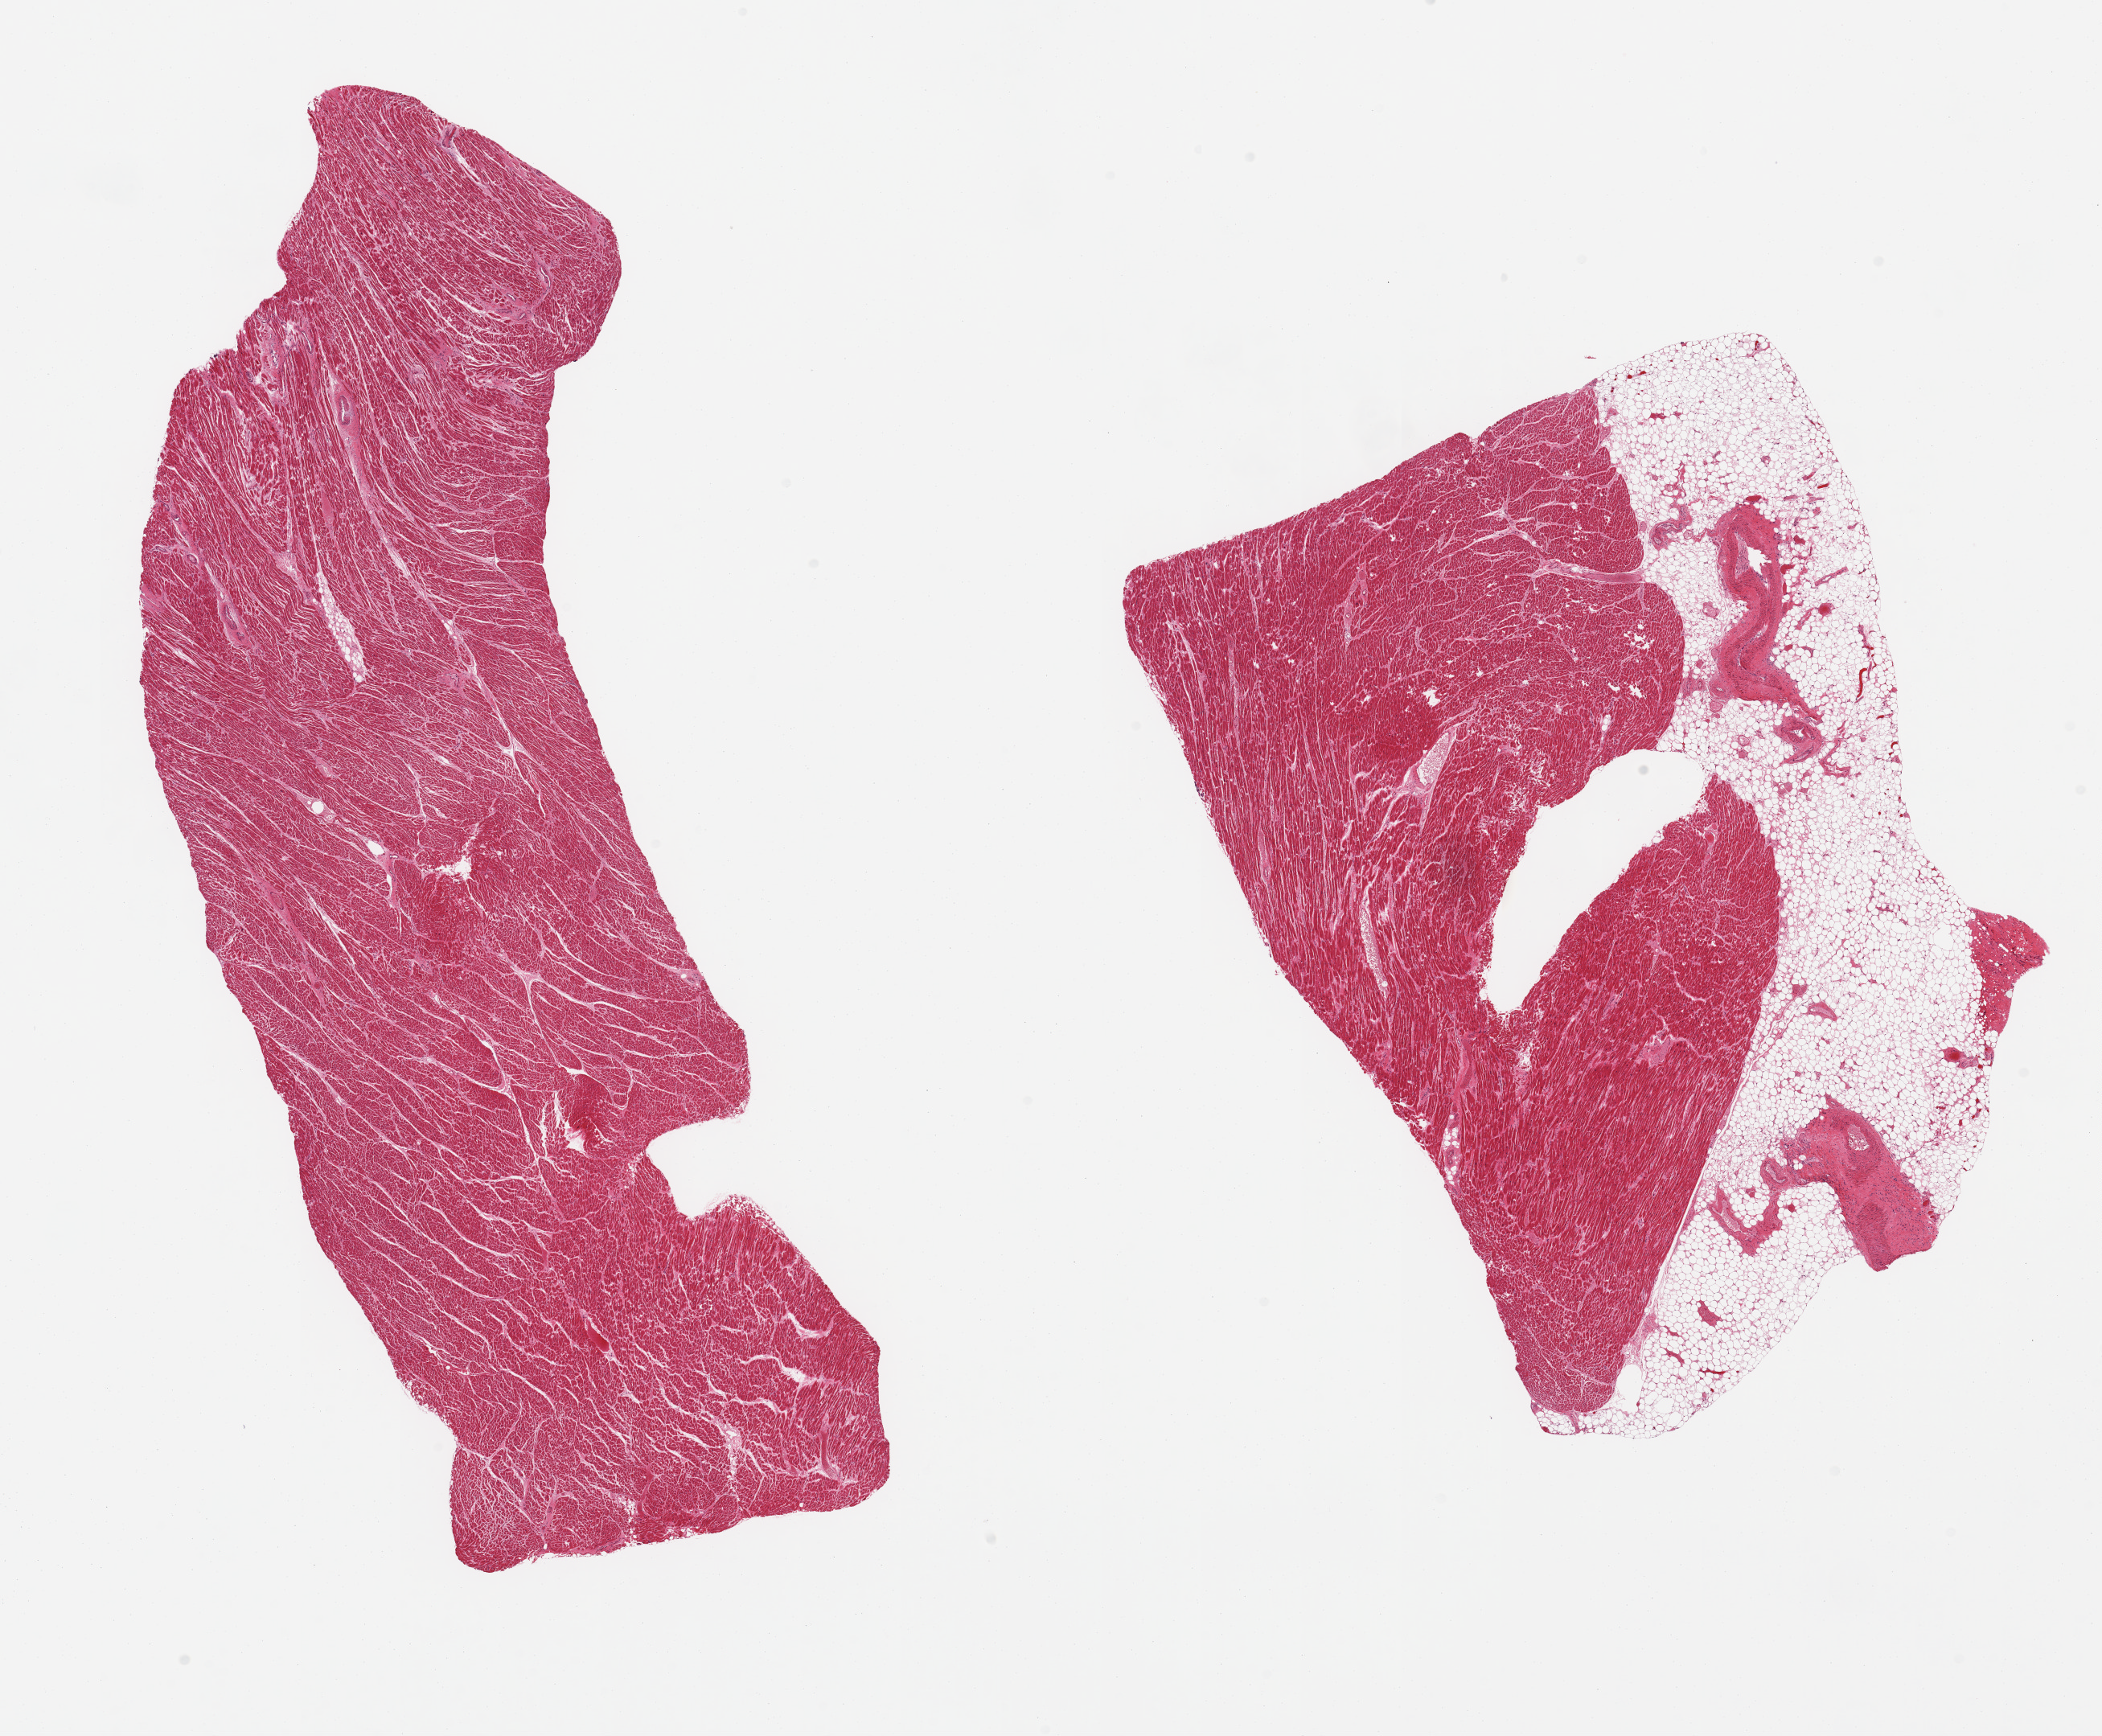
Digitized hematoxylin and eosin (H&E)-stained section — whole scanned area (about 20.7 x 17.1 mm, from a 20x scan) shown as a low-resolution overview. PAXgene-fixed paraffin-embedded (PFPE) section. Section of heart (target tissue). Tissue donor sample.
Reviewer comment on this tissue sample: 2 pieces; 1 with 40% external fat; hypereosinophilic areas consistent with ischemia.